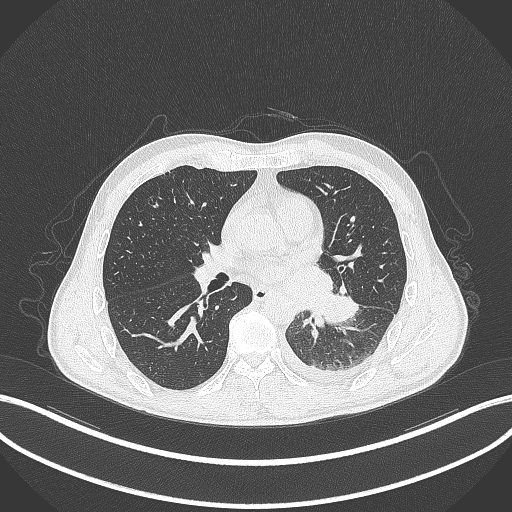
Chest CT, one axial slice. Slice 160 of 295 in the series (ordered by position). Lung window (W 1500 / L -600 HU). 1 mm slice thickness. 512 × 512 image matrix. Patient: male, 47 years. From the clinical record (not read from this slice): clinical TNM (as recorded): T3 N1 M1c.
Annotated regions visible in this slice (bounding box drawn by a radiologist):
- lung tumour (recorded histology: small cell carcinoma): bounding box <311,287,363,331> (left, top, right, bottom; pixels)